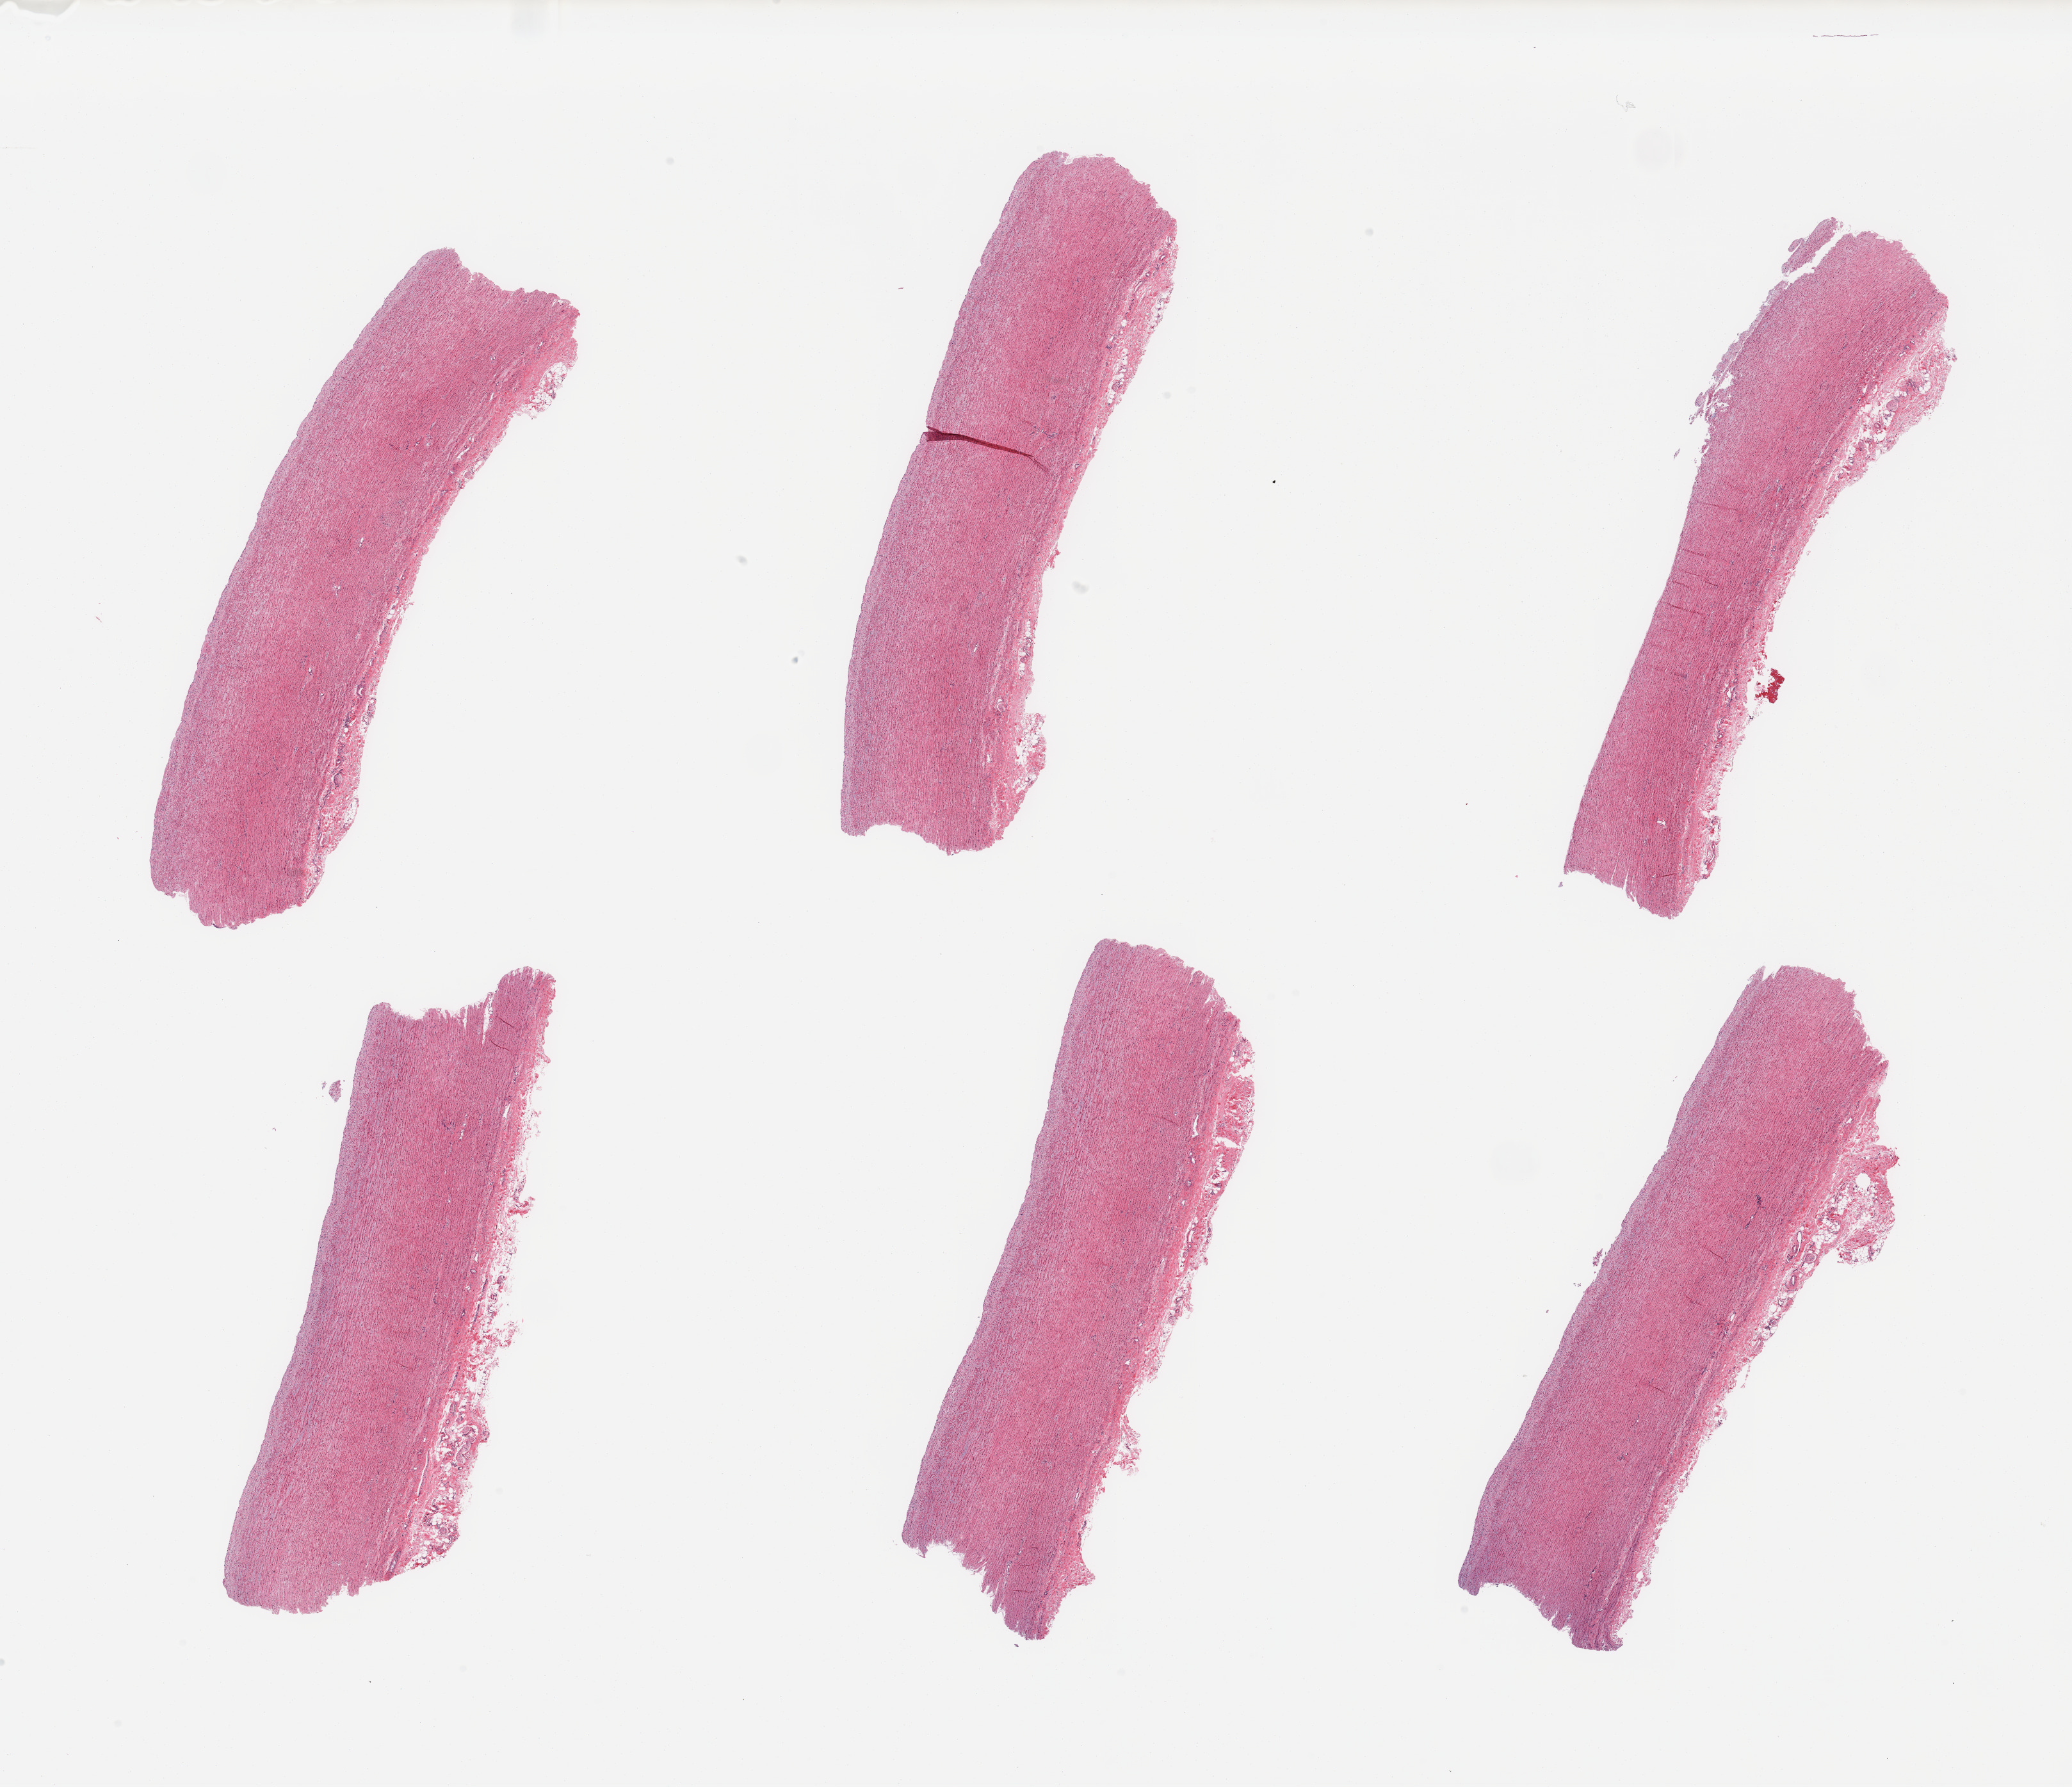
Digitized H&E-stained section, low-resolution overview of the scanned area, about 25.6 x 22.1 mm, PAXgene-fixed, paraffin-embedded tissue, section of aorta (target tissue), donor tissue sample.
Reviewer comment on this tissue sample: 6 pieces; ~1.0mm attached adventitia.